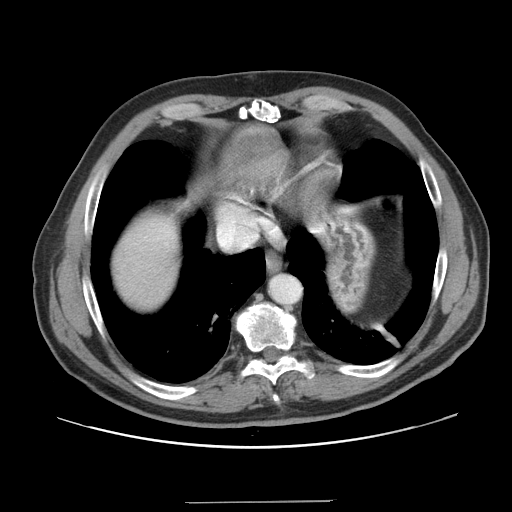
Contrast-enhanced abdominal CT, one axial slice; position 142 of 151 along the scan axis; 120 kVp; intravenous contrast given; soft-tissue window (W 400 / L 40 HU); 2.5 mm slice thickness; 512 × 512 image matrix, field of view 399 × 399 mm. Male patient, age 63 years. From the clinical record (not read from this slice): diagnosis: colorectal cancer liver metastases, imaged before liver resection; multiple liver metastases: no; largest metastasis: 2.1 cm; disease in both lobes: no.
Structures marked on this image (manually delineated by an expert):
- hepatic veins: bounding box <219,217,258,248> (left, top, right, bottom; pixels)
- liver: <111,218,182,312>
- planned liver remnant (the part of the liver to remain after resection): <108,217,182,312>